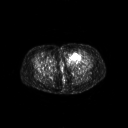
FDG PET of an extremity soft-tissue mass (from a PET/CT study), one axial slice; position 37 of 267 along the scan axis; 3.27 mm slice thickness; 128 × 128 image matrix, field of view 700 × 700 mm. Female patient, age 47 years. From the clinical record (not read from this slice): histological type: myxofibrosarcoma; grade: intermediate; site of the primary tumour: left thigh.
Structures marked on this image (expert contour drawn on MRI and transferred to this co-registered scan by the dataset authors):
- gross tumour volume including surrounding oedema: box from (x=66, y=52) to (x=83, y=65) px
- gross tumour volume (mass): (x=66, y=52)–(x=81, y=62)